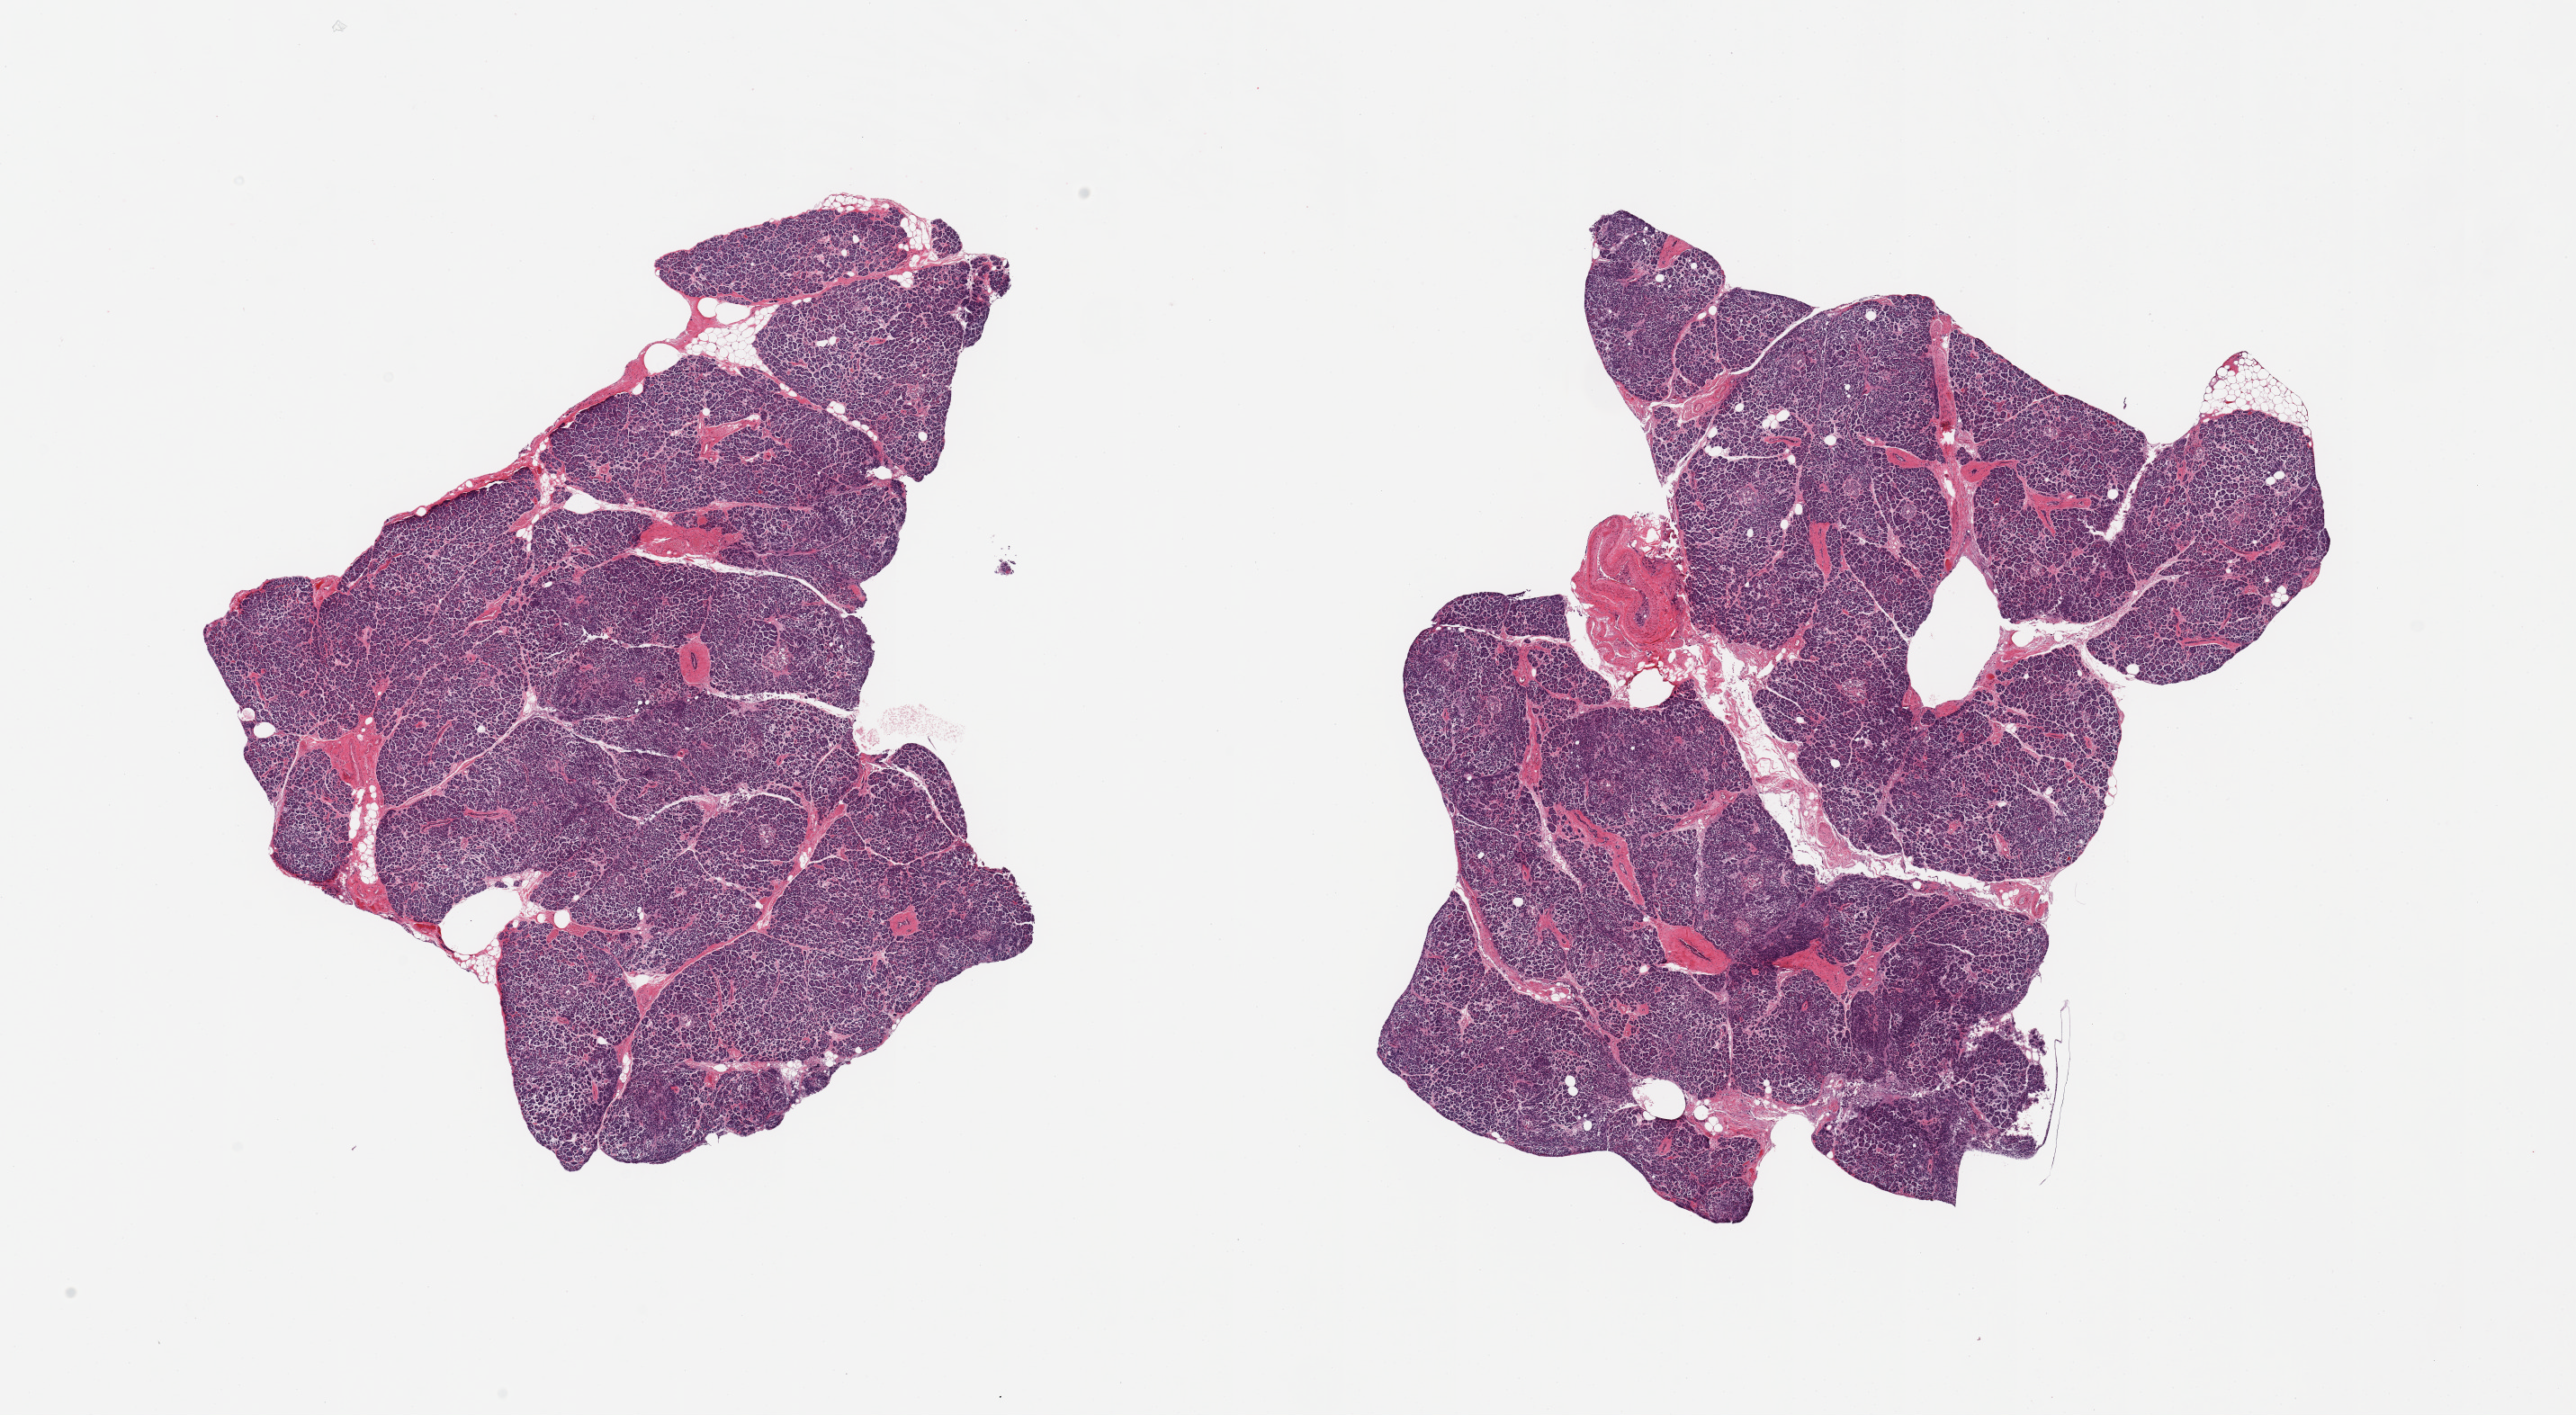
Whole-slide image, H&E stain, whole scanned area (about 22.6 x 12.4 mm) shown as a low-resolution overview, PAXgene-fixed, paraffin-embedded tissue, sampled site (target tissue): pancreas, tissue donor sample. Donor: female.
Review note (as recorded): 2 pieces; well trimmed.